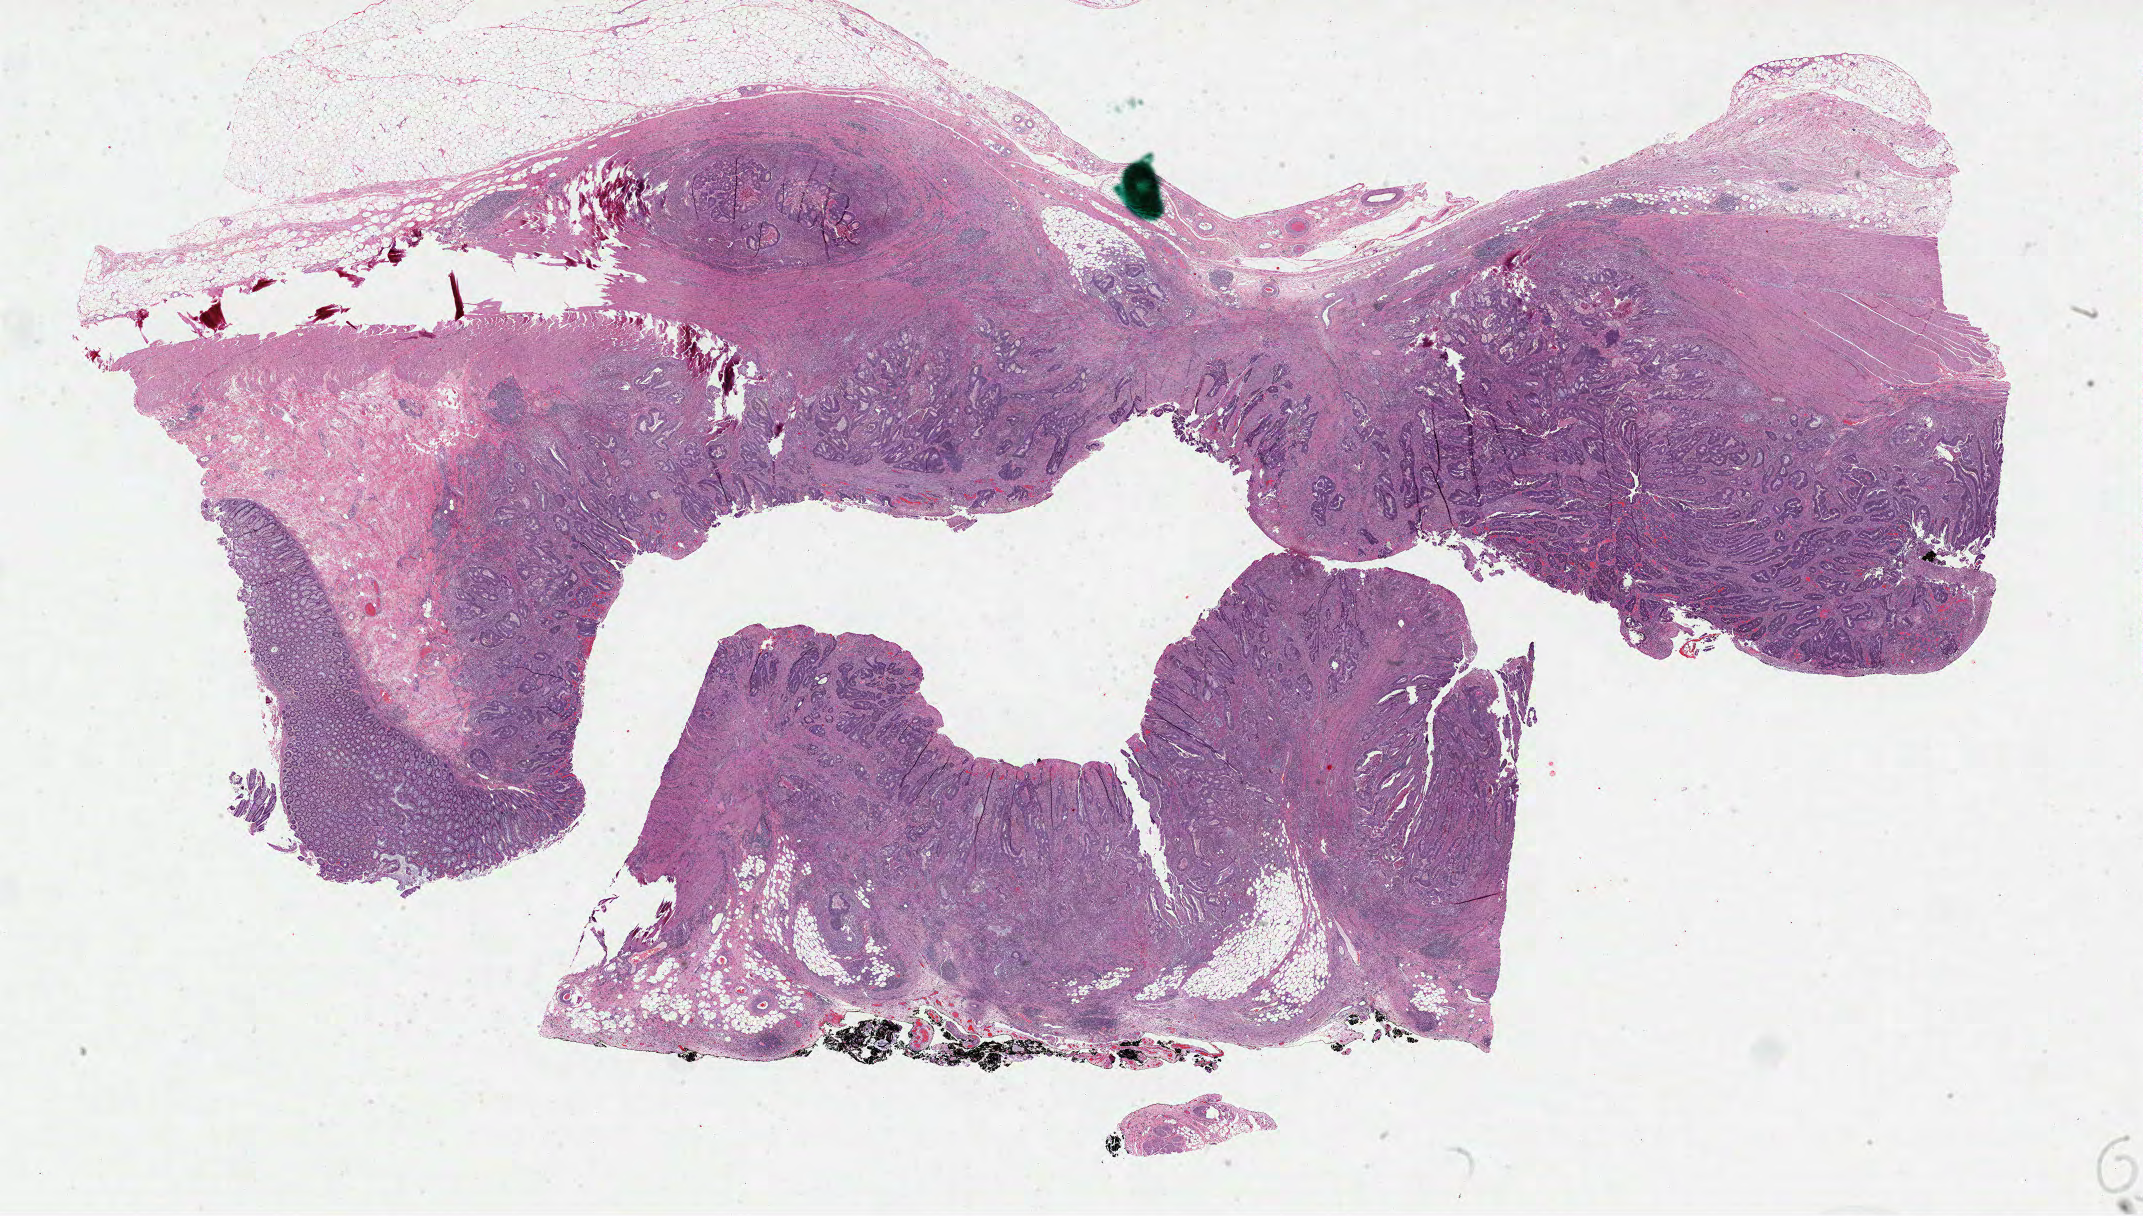
Digitized Hematoxylin and eosin (H&E) stained tissue section (whole slide) — whole scanned area (about 34.6 x 19.6 mm) shown as a low-resolution overview; FFPE section; sample: primary tumour, colon. Female patient; age at initial diagnosis 75 years.
- diagnosis: Adenocarcinoma, NOS (hepatic flexure of colon)
- lymph nodes positive (case pathology): 0 of 20 examined
- AJCC pathologic stage: IIA (7th edition)